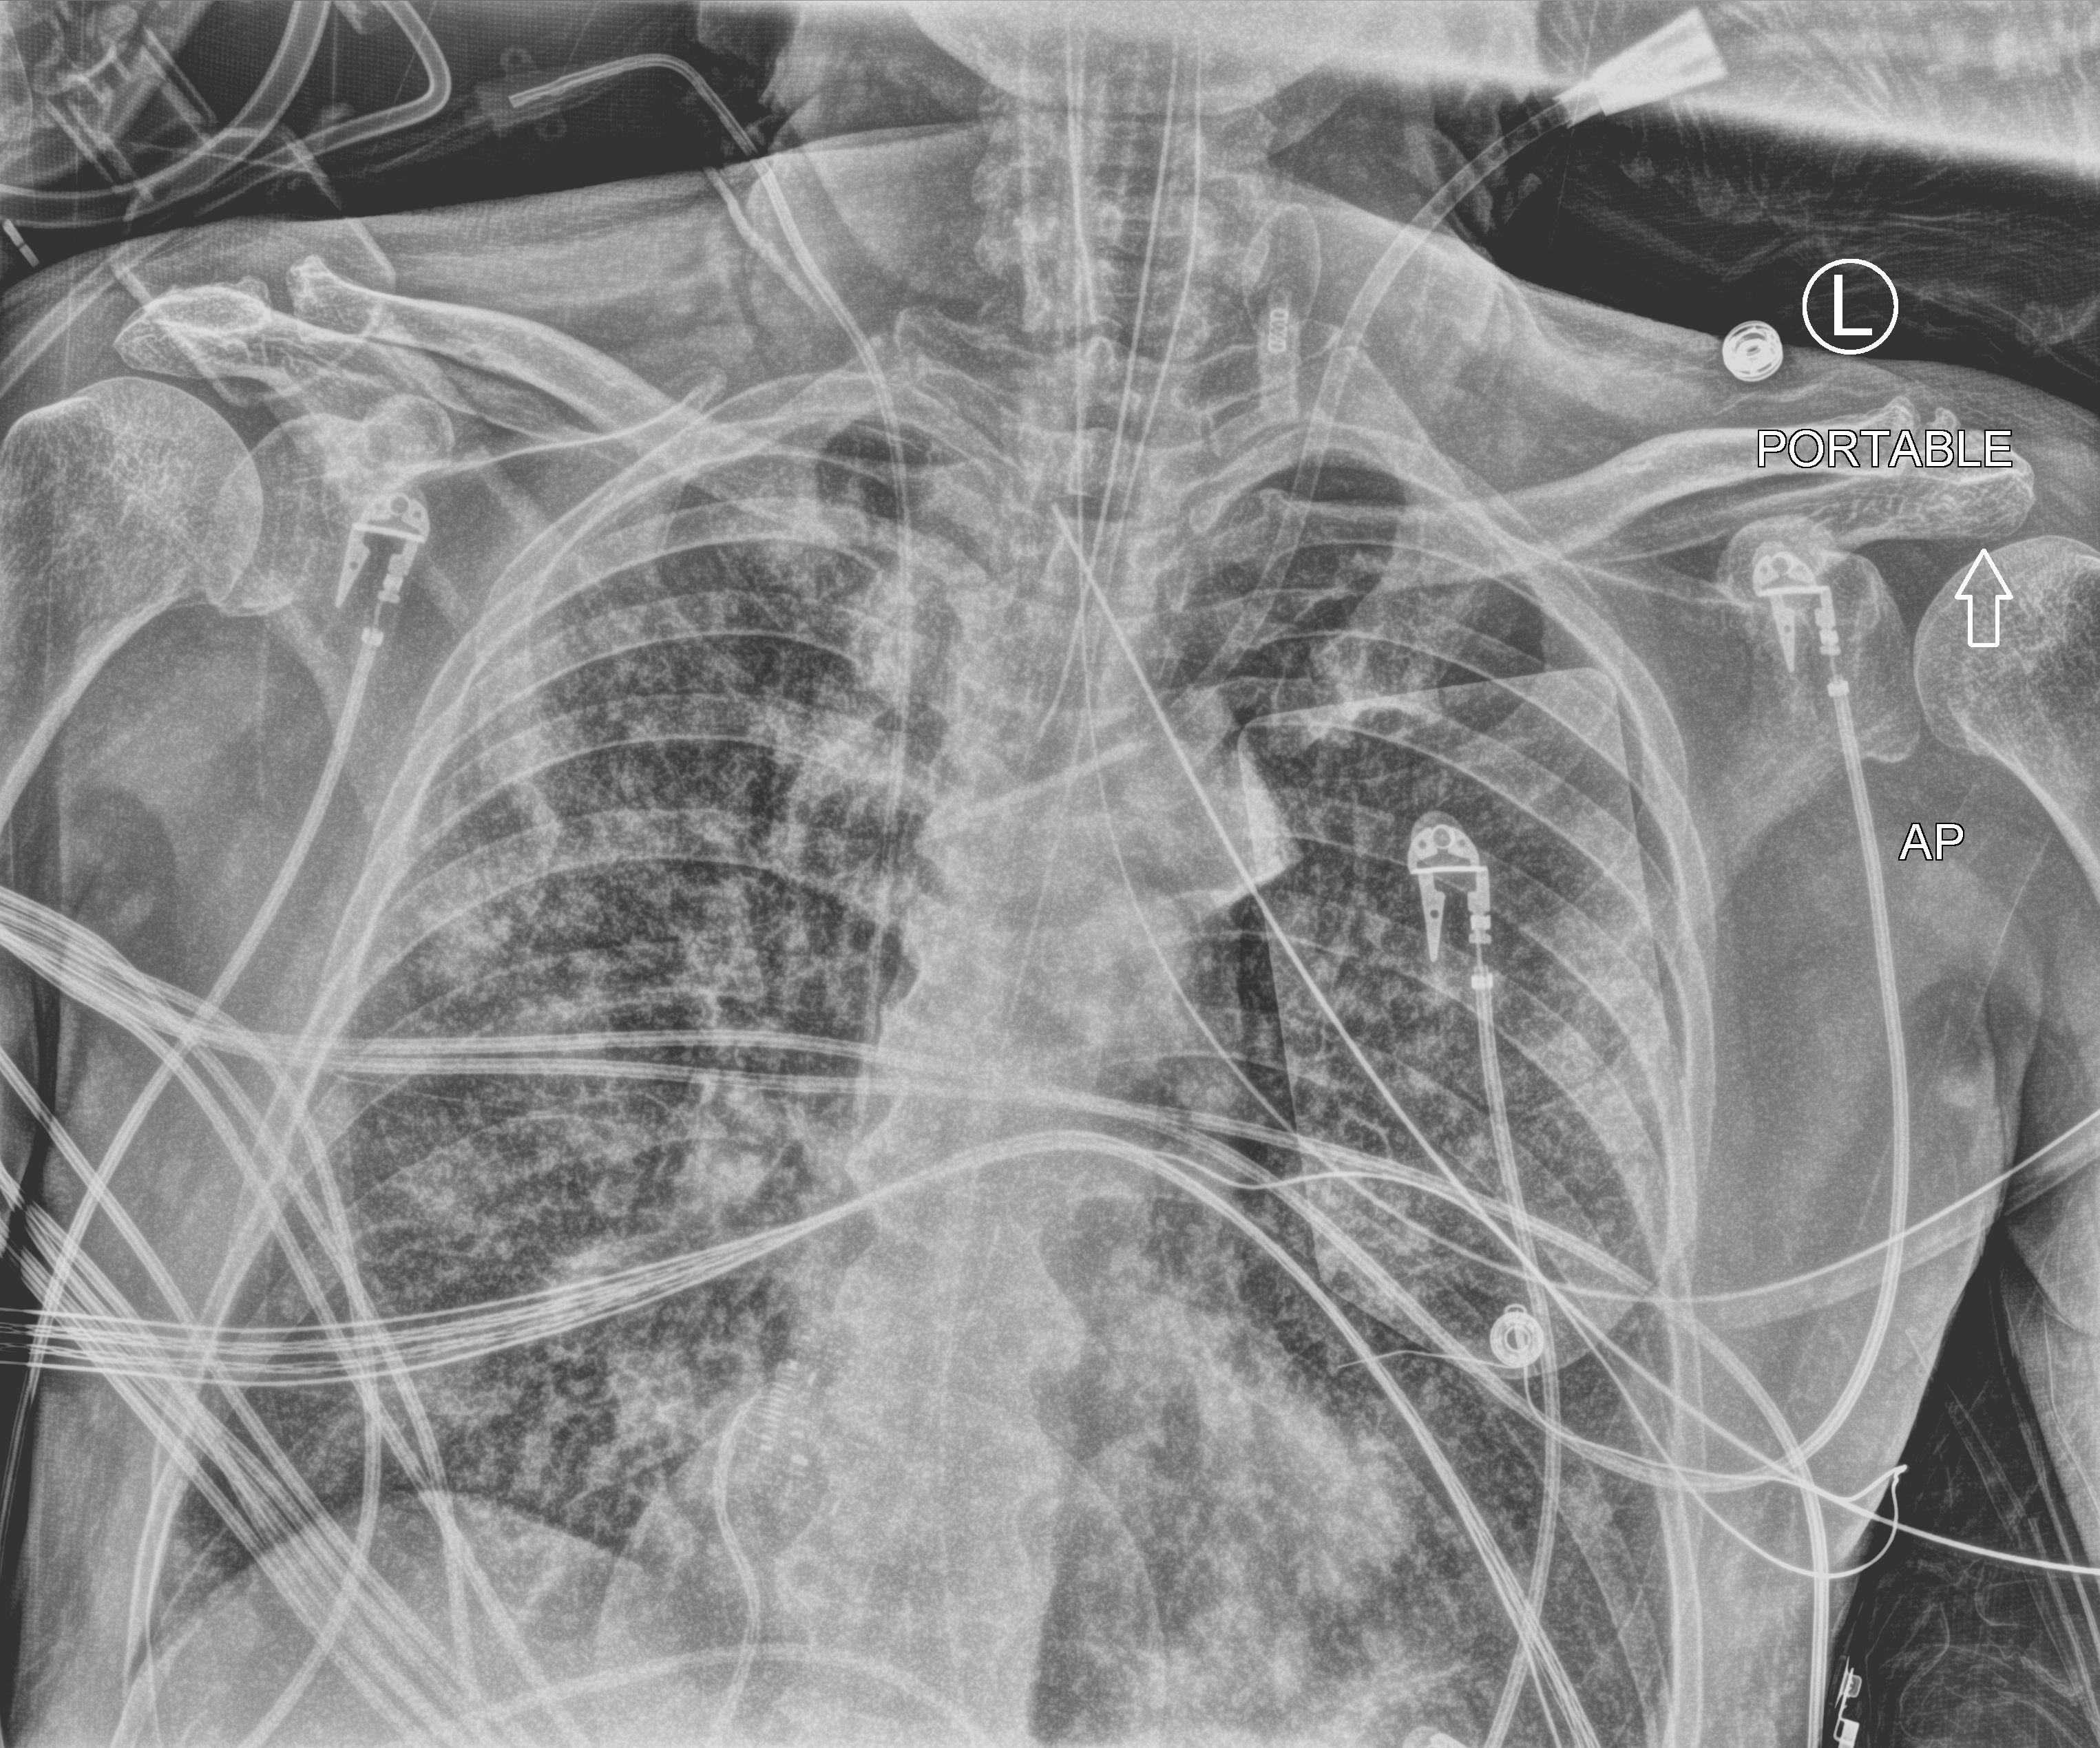
Bedside chest radiograph (computed radiography). Patient hospitalised with COVID-19; male, aged 60–74 years.
Admission-level facts for this patient (not findings on this image; timing relative to this image not recorded):
- length of hospital stay: 26 days
- chronic kidney disease (admission record): no
- admitted to intensive care during this hospital stay: yes